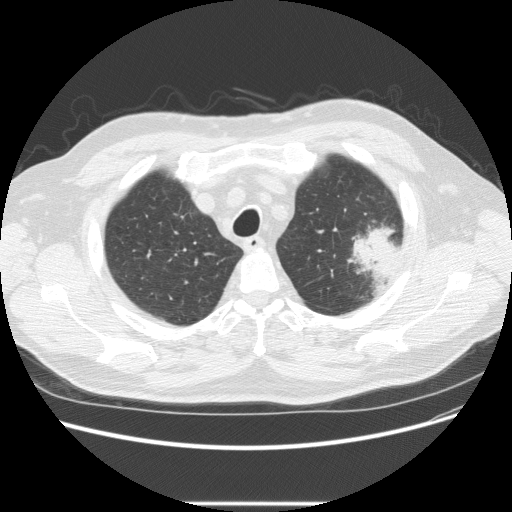
Low-dose screening chest CT, one axial slice; slice 188 of 233 in the series (ordered by position); reconstruction kernel STANDARD; 120 kVp; lung window (W 1500 / L -600 HU); 2.5 mm slice thickness; 512 × 512 image matrix, field of view 380 × 380 mm.
Outlined on this slice (manually delineated by an expert):
- lesion 1 (tumor, upper lobe of left lung): bounding box [x1, y1, x2, y2] px = [347, 223, 401, 286]